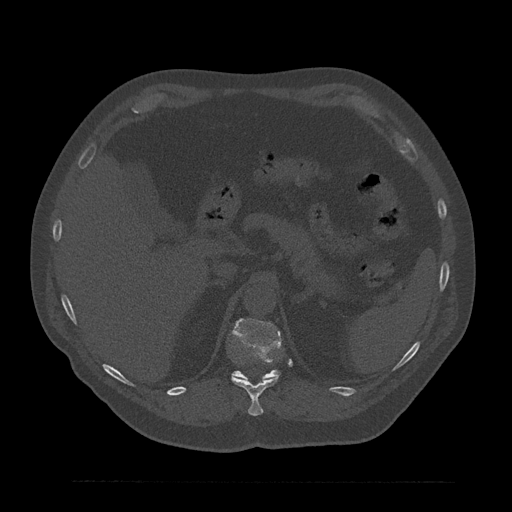
CT including the spine, one axial slice; slice 265 of 797 in the series (ordered by position); reconstruction kernel Br40s/3; 120 kVp; bone window (W 1800 / L 400 HU); 0.5 mm slice thickness; 512 × 512 image matrix, field of view 430 × 430 mm. Male patient, age 61 years. Case-level facts recorded for this patient, not image findings: primary cancer: prostate.
Annotated regions visible in this slice (semi-automatic segmentation, software-assisted and operator-edited):
- T11 vertebra: bounding box <231,375,279,416> (left, top, right, bottom; pixels)
- T12 vertebra: <232,318,281,381>